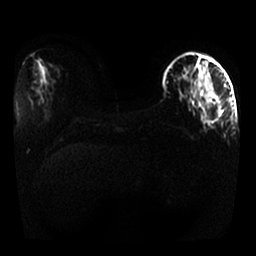
Breast MRI, one axial slice; position 10 of 25 along the scan axis; diffusion-weighted series; image 2 of 4 stored at this slice position (different b-values; order by instance number); 1.5 T; 256 × 256 image matrix, field of view 330 × 330 mm. Female patient.
Outlined on this slice (expert manual segmentation):
- tumour on diffusion-weighted imaging: bounding box <205,91,218,104> (left, top, right, bottom; pixels)